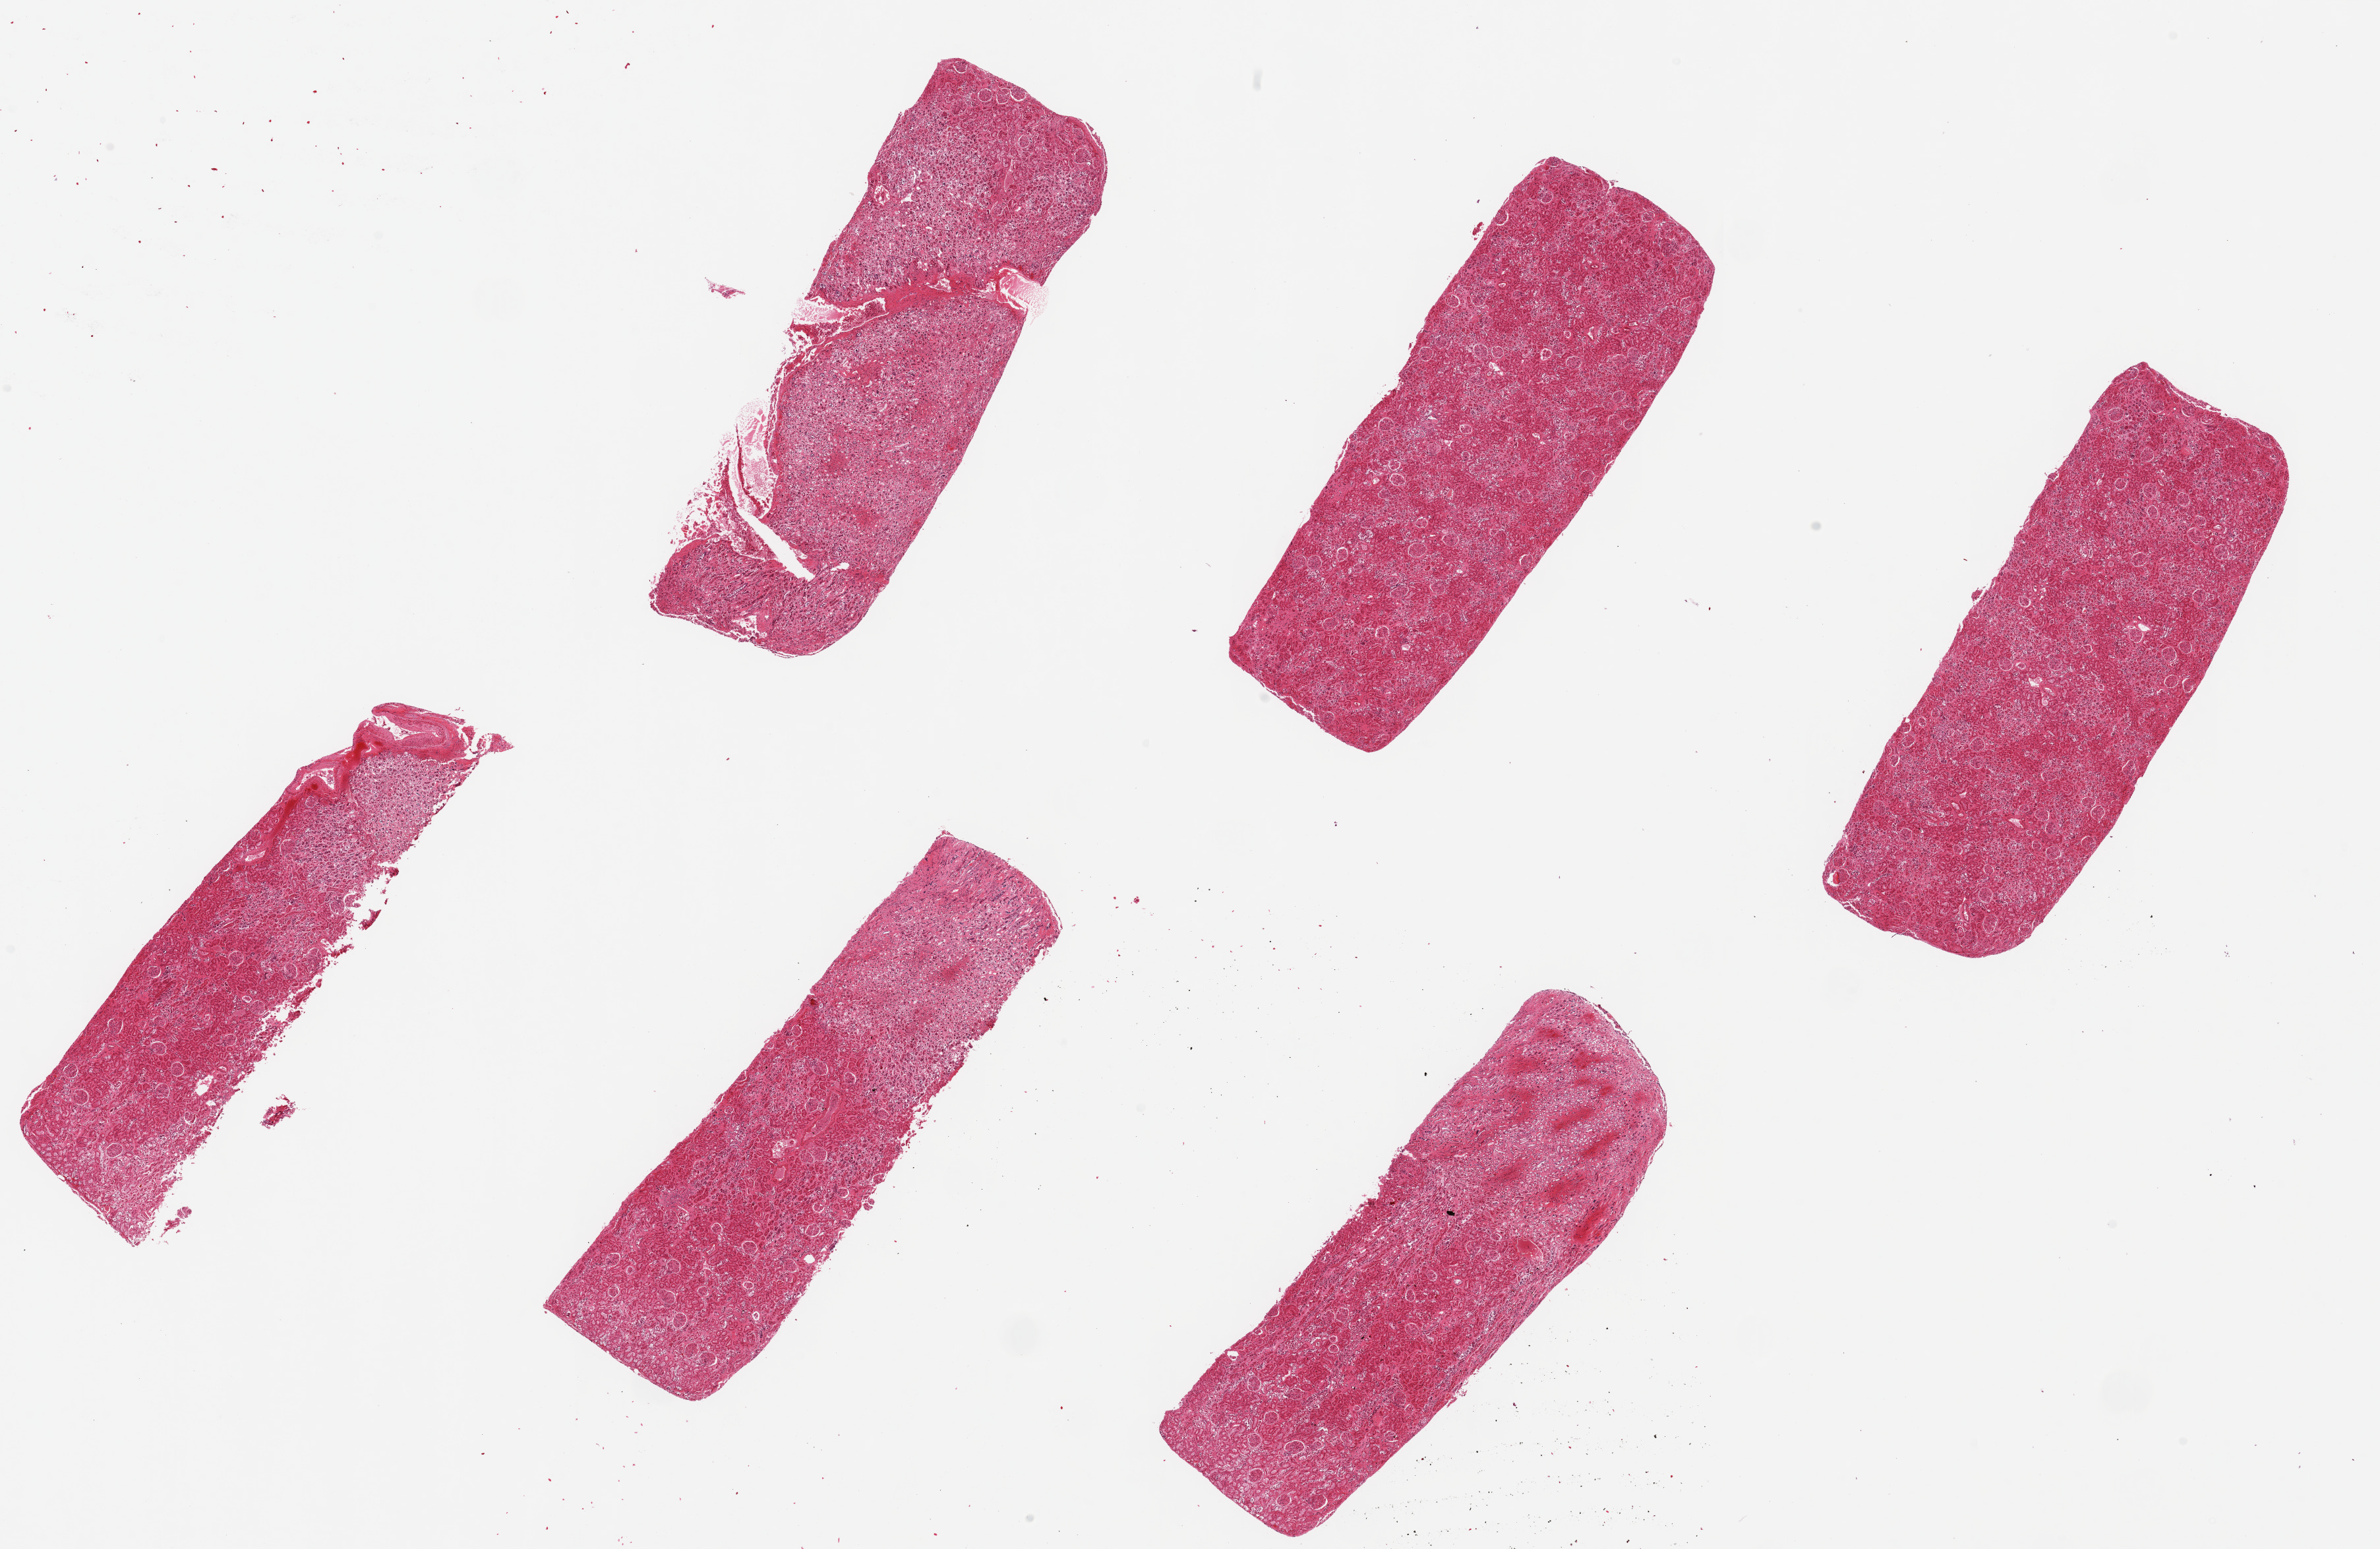
Hematoxylin and eosin (H&E) whole-slide image, a low-resolution overview of the entire scanned area, about 28.5 x 18.6 mm (from a 20x scan). PAXgene-fixed paraffin-embedded (PFPE) section. Section of renal cortex (target tissue). Donor tissue sample. Male donor.
Pathologist's review note for this sample: 6 pieces, up to 7.5x2.5mm; no chronic lesions, some hyperemia; 1 piece mostly medulla, other pieces have medulla (marked on image).